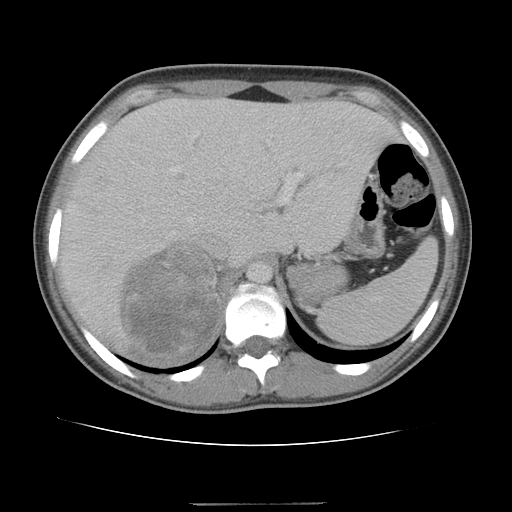
Contrast-enhanced abdominal CT, one axial slice; position 79 of 100 along the scan axis; intravenous contrast given; soft-tissue window (W 400 / L 40 HU); 512 × 512 image matrix. Patient: female, 21 years. From the clinical record (not read from this slice): diagnosis: adrenocortical carcinoma; tumour side: right adrenal; tumour size at pathology: 15.5 cm; Ki-67 index: 26 %; stage (as recorded): 3.
Outlined on this slice (semi-automatic segmentation, software-assisted and operator-edited):
- mass: bounding box [x1, y1, x2, y2] px = [122, 245, 217, 350]